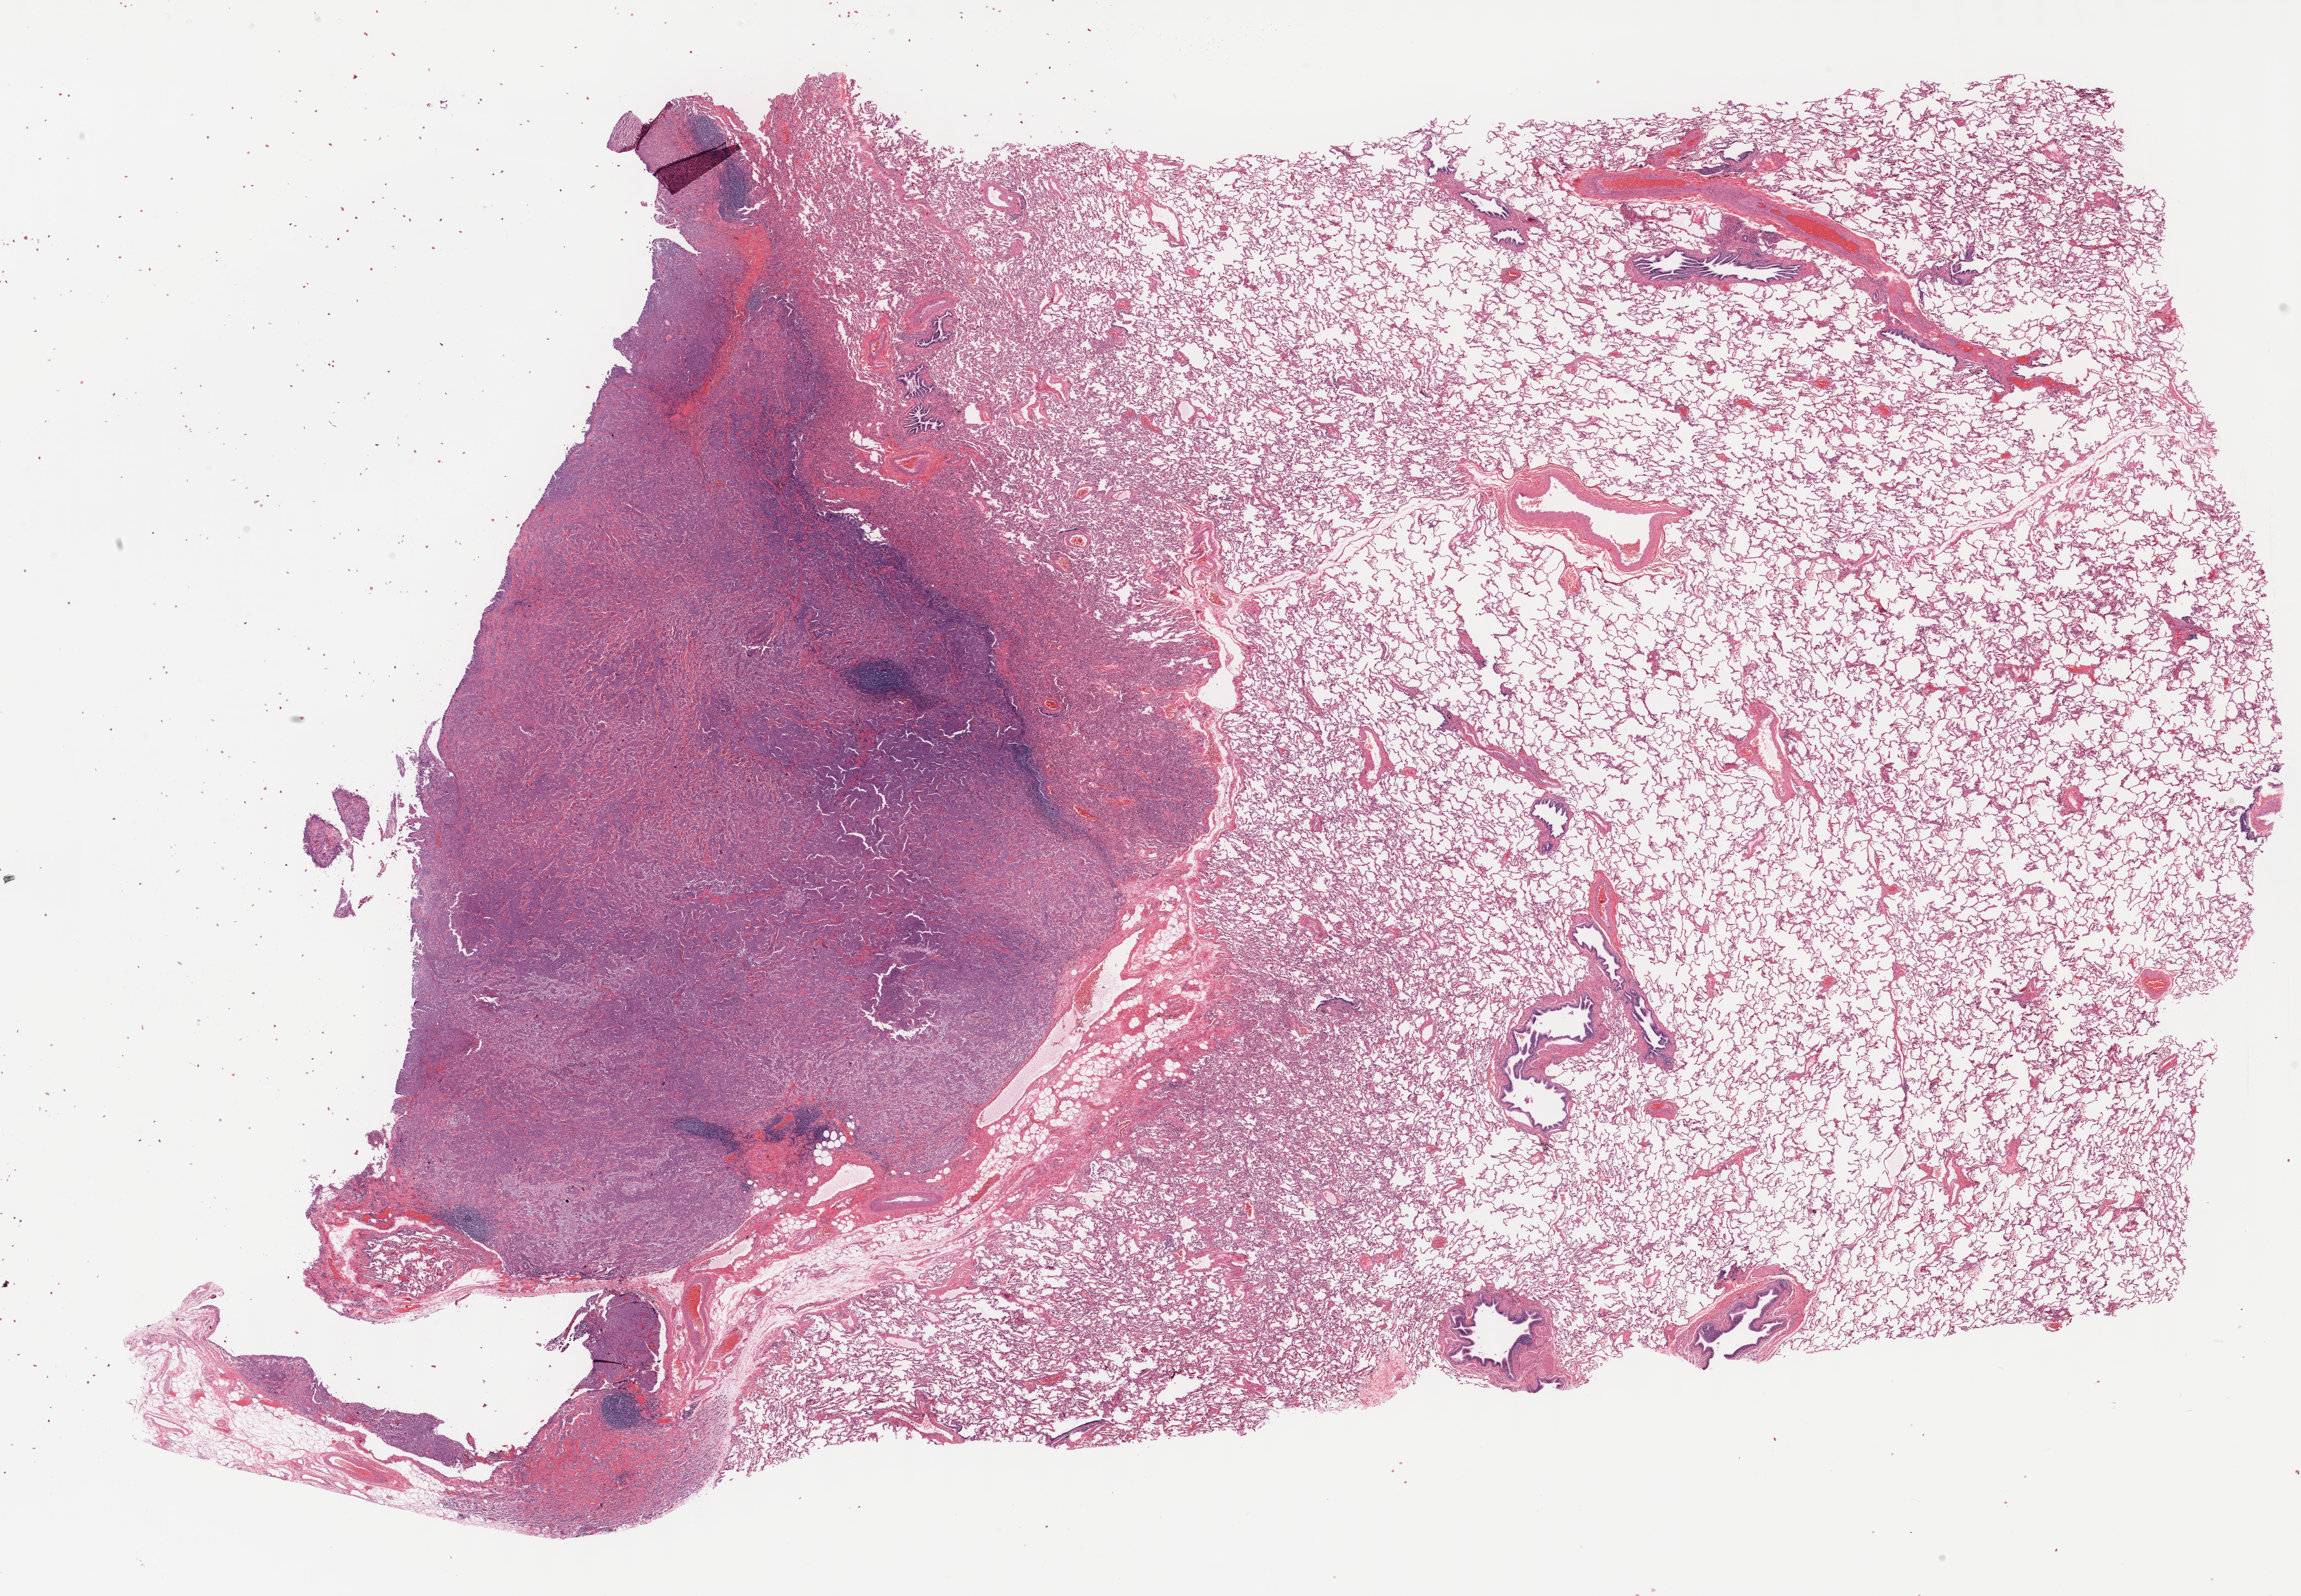
H&E-stained whole-slide image, shown as a low-resolution overview of the whole scanned area (about 28.7 x 19.9 mm); formalin-fixed paraffin-embedded (FFPE) diagnostic section; sample: primary tumour, mesothelium. Patient: male, age at initial diagnosis 36 years.
Histologic diagnosis: Epithelioid mesothelioma, malignant (pleura, NOS).